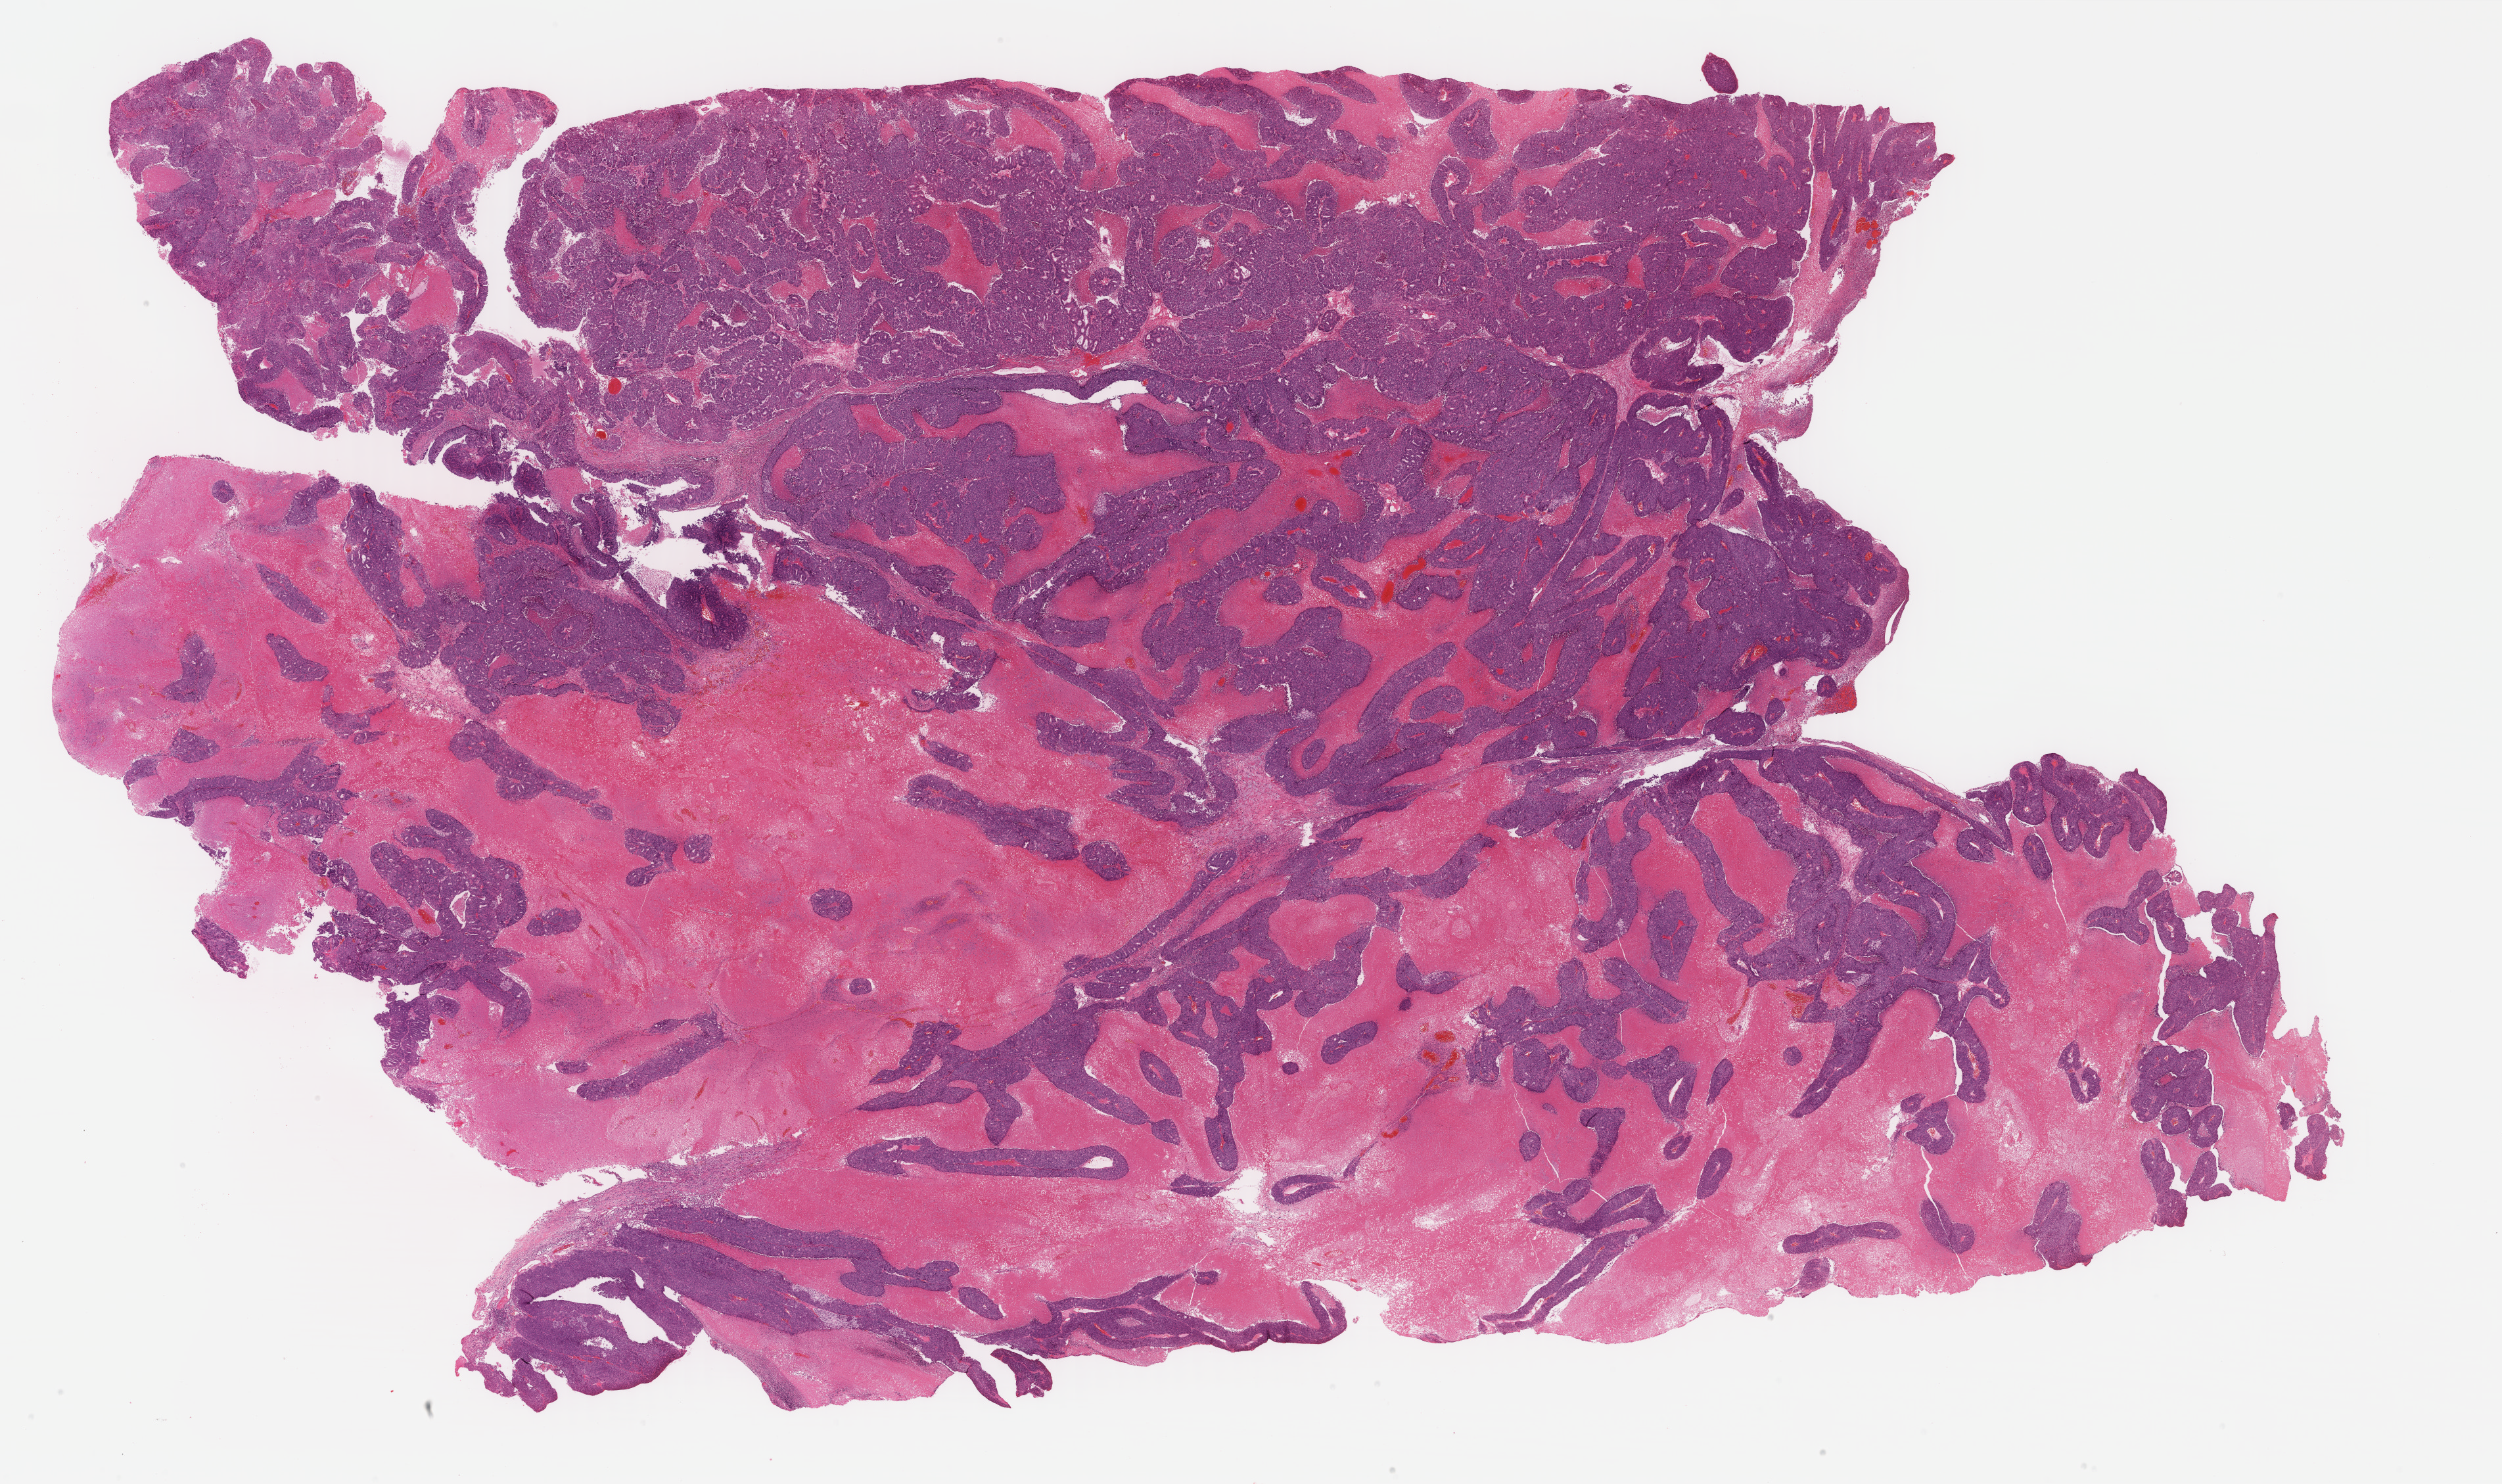
Digitized Hematoxylin and eosin (H&E) stained tissue section (whole slide) — low-resolution overview of the scanned area, about 30.2 x 17.9 mm (acquisition: 40x scan). FFPE section. Sample: primary tumour, uterus. Female patient; age at initial diagnosis 76 years. Histologic grade: G3 (poorly differentiated).
FIGO stage: IA. Diagnosis: Endometrioid adenocarcinoma, NOS (endometrium).